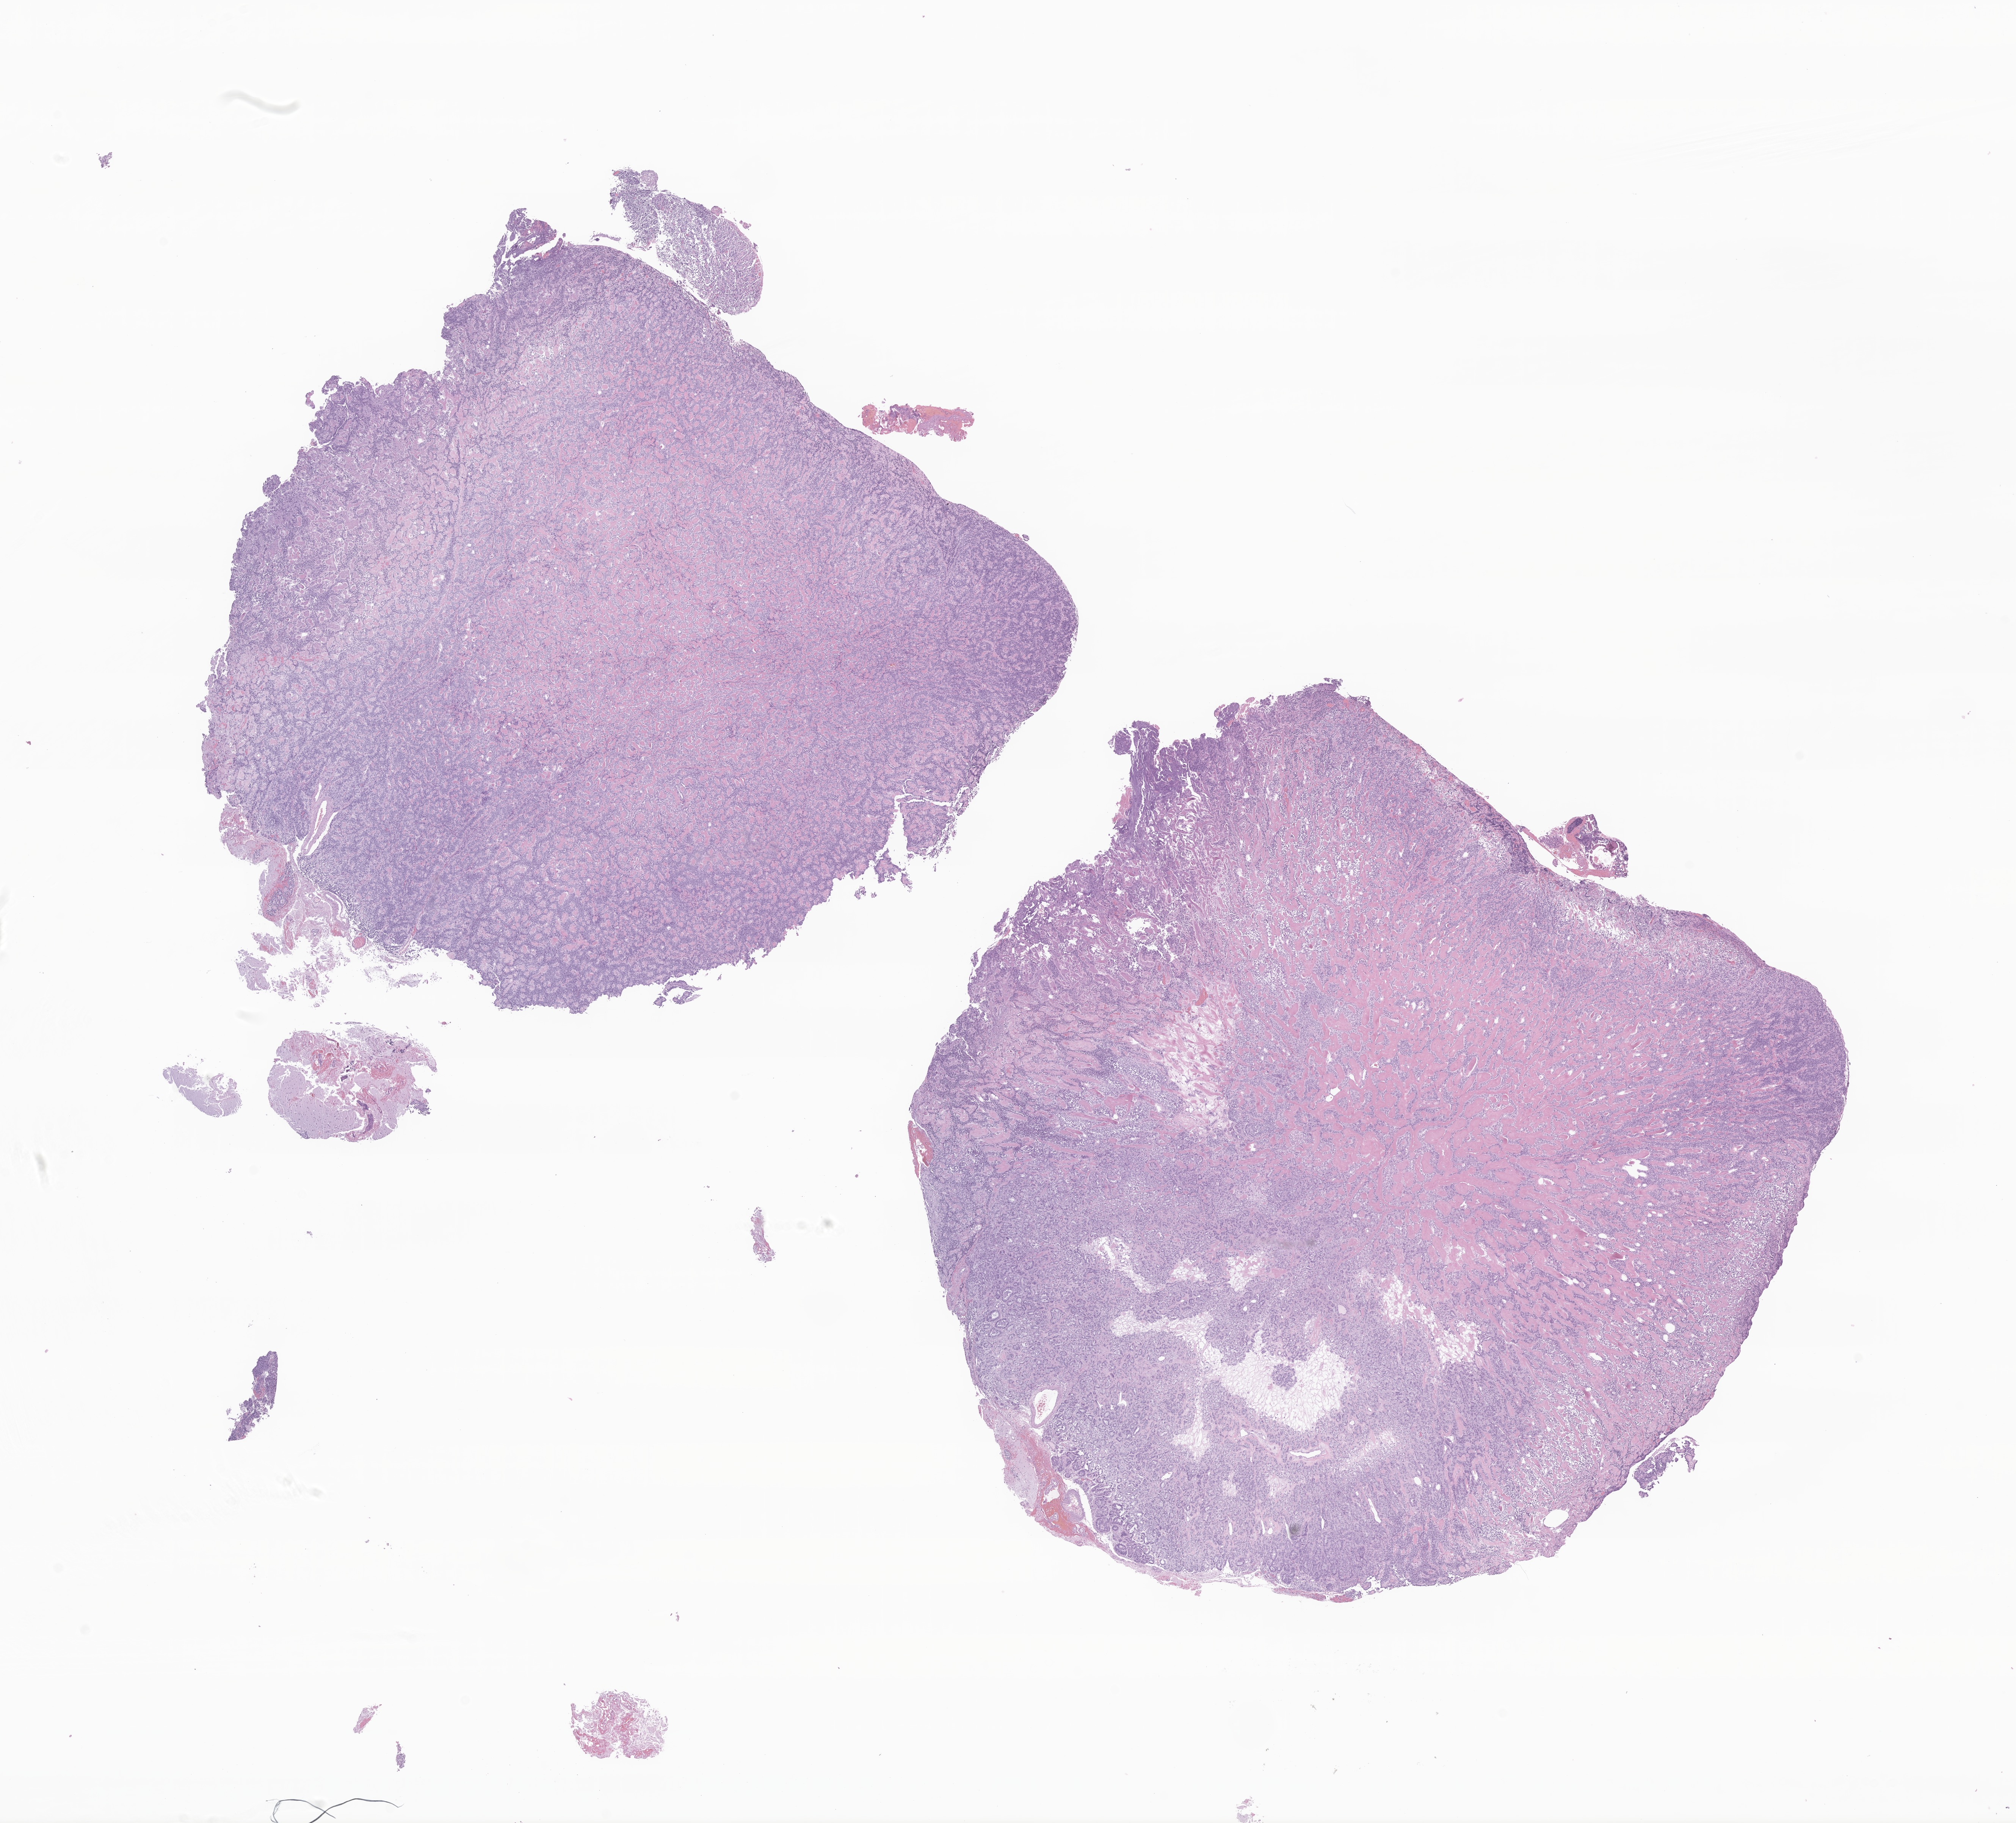
Whole-slide image, hematoxylin and eosin (H&E) stain of tumor tissue from the brain — whole scanned area (about 22.4 x 20.3 mm) shown as a low-resolution overview, formalin-fixed, paraffin-embedded (FFPE) tissue. Female patient, age 179 months (14 years 11 months).
Recorded diagnosis: Neoplasm, malignant.